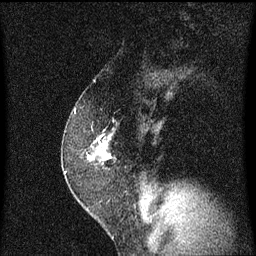
Breast MRI (dynamic contrast-enhanced), one sagittal slice; position 41 of 60 along the scan axis; dynamic contrast-enhanced series, image 2 of 3 at this slice position (ordered by acquisition); 1.5 T; TE 4.2 ms, TR 8.4 ms; 256 × 256 image matrix, field of view 200 × 200 mm. Patient: female, 52 years. Case-level facts recorded for this patient, not image findings: setting: breast cancer imaged before/during neoadjuvant chemotherapy; receptor status: HER2-positive.
Annotated regions visible in this slice (semi-automatically segmented with operator editing):
- analysis volume of interest (the breast-tissue region the enhancement analysis was run in; not a lesion): bounding box <63,124,113,191> (left, top, right, bottom; pixels)
- tumour enhancement mask (voxels above the 70 % enhancement threshold inside the analysis volume of interest): <90,138,109,161>